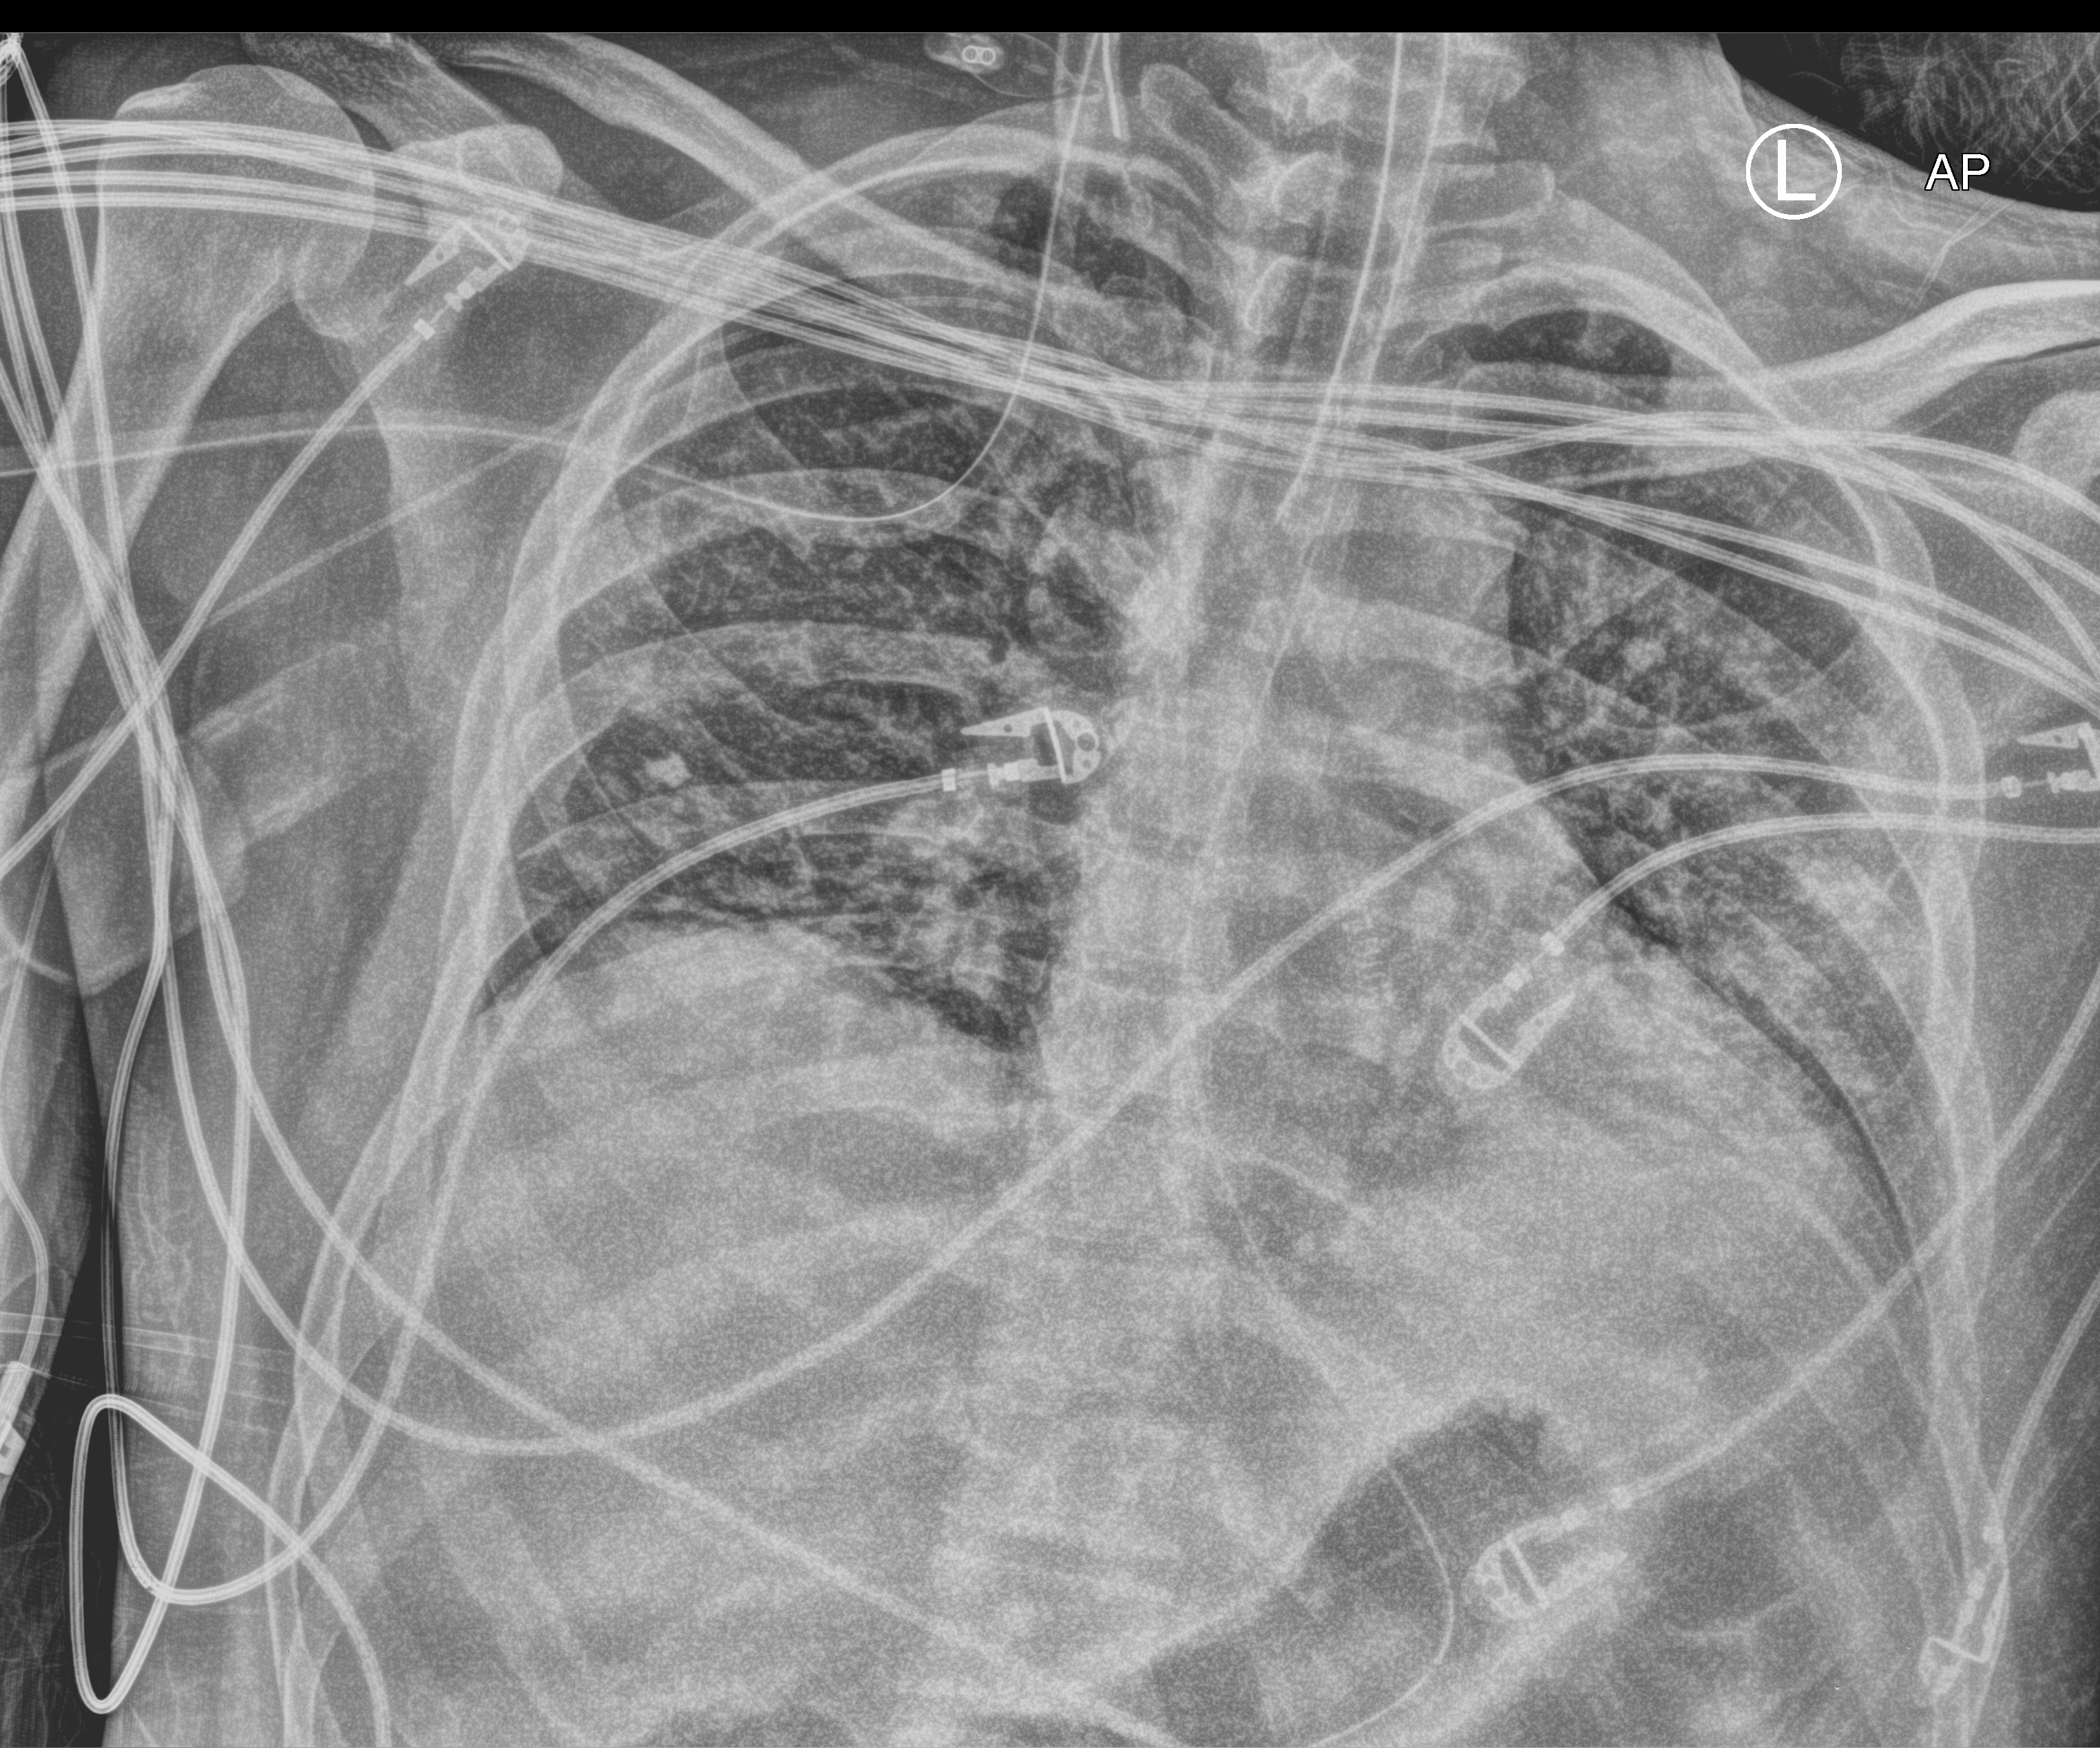
Portable chest radiograph. Patient hospitalised with COVID-19; male, aged 18–59 years.
Hospital-stay facts (about this admission, not read from this image; timing relative to this image not recorded): admitted to intensive care during this hospital stay: no; diabetes (admission record): no; mechanically ventilated during this hospital stay: yes.